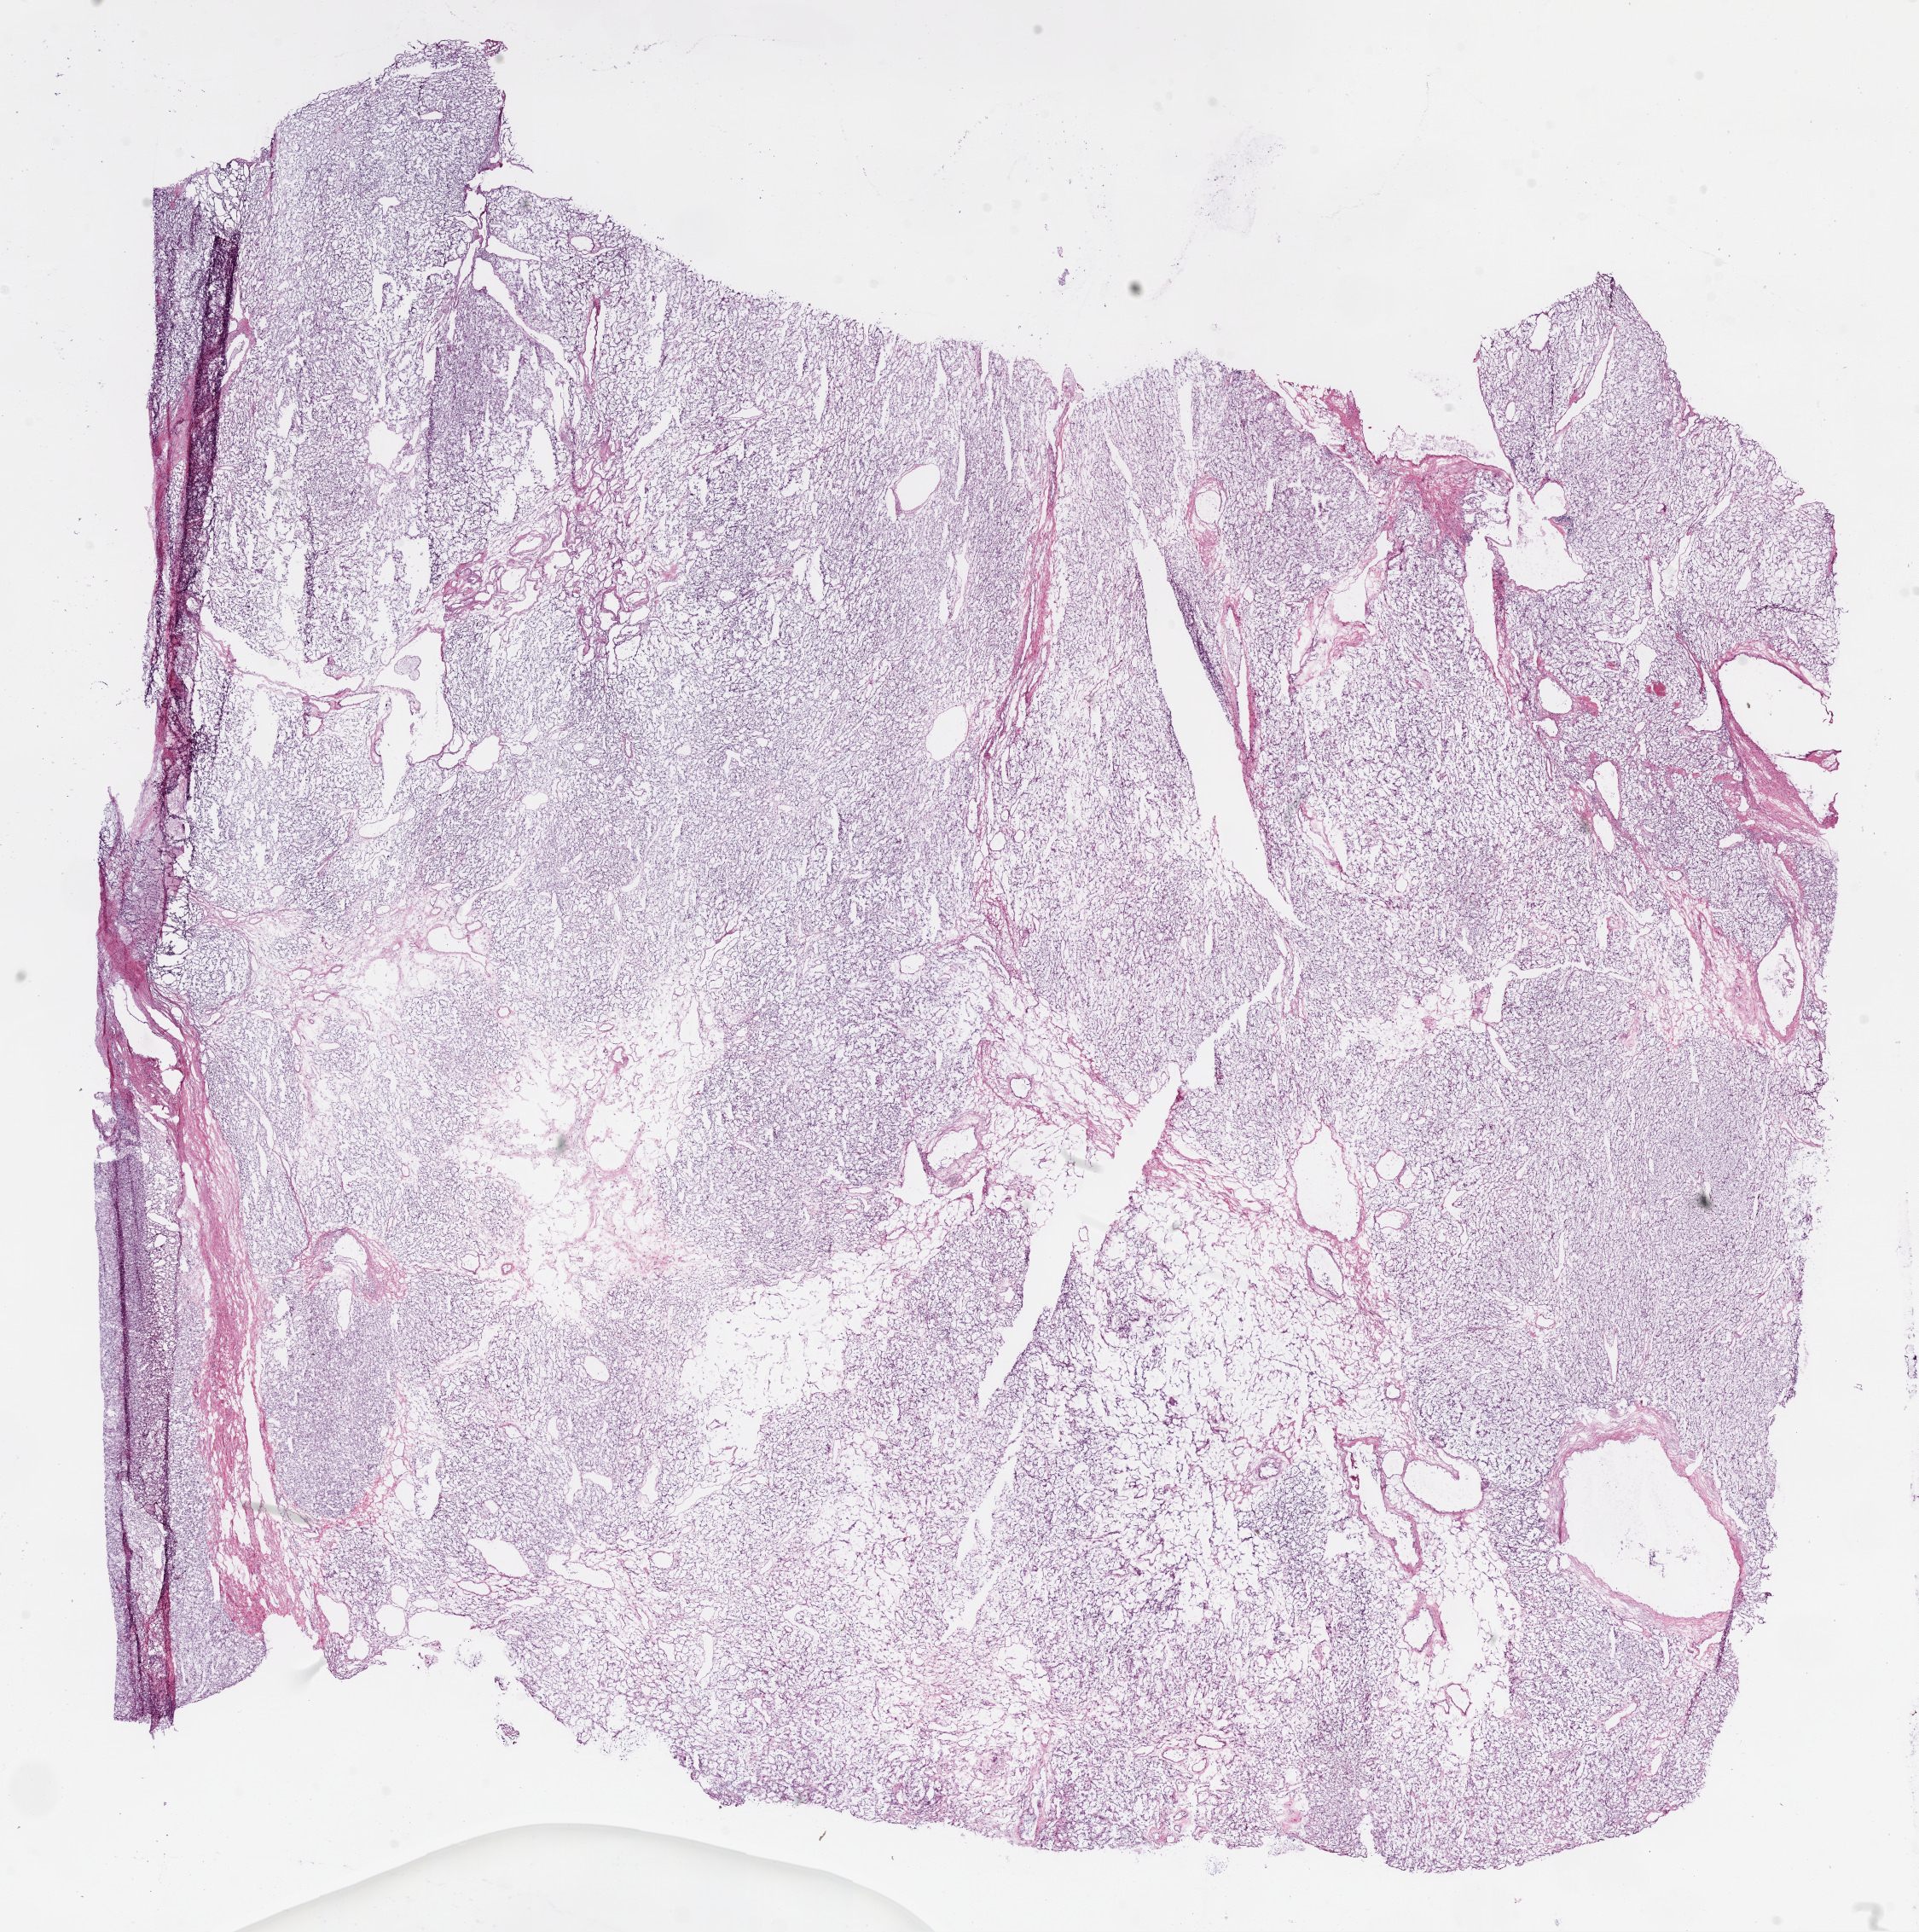
Hematoxylin and eosin (H&E) stained whole-slide image, shown as a low-resolution overview of the whole scanned area (about 18.1 x 18.2 mm, slide scanned at 20x), frozen section from the bottom of the tissue portion, kidney, primary tumour sample. Female, age 59 years at initial diagnosis. Histologic grade: G4 (undifferentiated). Pathologist review of this section (percent, as recorded): tumour cells 90%, tumour nuclei 85%, normal cells 0%, stromal cells 10%, necrosis 0%.
AJCC pathologic stage: III. Histologic diagnosis: Clear cell adenocarcinoma, NOS. Laterality: left.